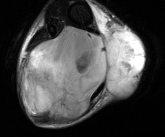
MRI of an extremity soft-tissue mass, one axial slice; position 34 of 81 along the scan axis; T2-weighted fat-saturated; MR volume resampled by the dataset authors to the PET/CT grid (not the native acquisition matrix); 165 × 137 image matrix. Male patient. Case-level facts recorded for this patient, not image findings: histological type: liposarcoma - round cell; grade: high; site of the primary tumour: right calf.
Outlined on this slice (expert contour drawn on MRI and transferred to this co-registered scan by the dataset authors):
- gross tumour volume (mass): box from (x=19, y=25) to (x=145, y=120) px